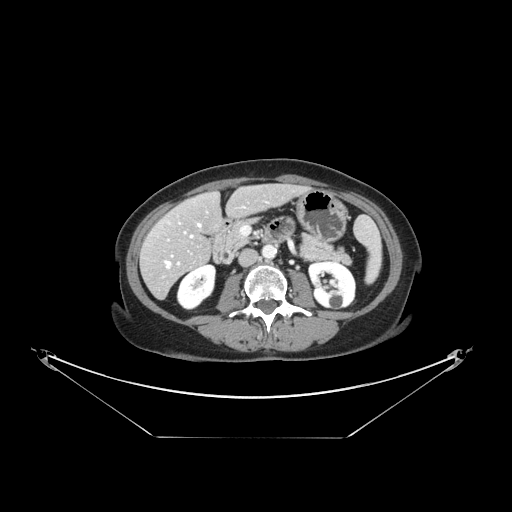
Contrast-enhanced abdominal CT, one axial slice; position 55 of 148 along the scan axis; 120 kVp; intravenous contrast given; soft-tissue window (W 400 / L 40 HU); 2.5 mm slice thickness; 512 × 512 image matrix, field of view 500 × 500 mm. Female patient, age 73 years. Case-level facts recorded for this patient, not image findings: diagnosis: colorectal cancer liver metastases, imaged before liver resection; multiple liver metastases: no; largest metastasis: 1 cm; disease in both lobes: no.
Annotated regions visible in this slice (expert manual segmentation):
- hepatic veins: bounding box (x1, y1, x2, y2) in pixels: (165, 222, 201, 268)
- liver: (142, 185, 301, 297)
- planned liver remnant (the part of the liver to remain after resection): (164, 185, 301, 248)